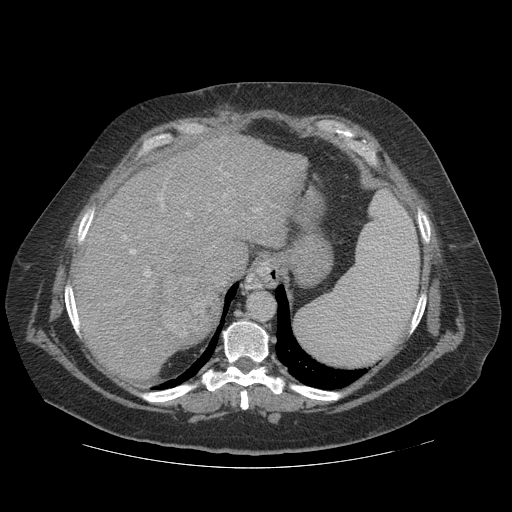
Contrast-enhanced abdominal CT (liver protocol), one axial slice. Position 90 of 121 along the scan axis. 140 kVp. Soft-tissue window (W 400 / L 40 HU). 2.5 mm slice thickness. 512 × 512 image matrix, field of view 420 × 420 mm. Case-level facts recorded for this patient, not image findings: diagnosis: hepatocellular carcinoma (patient treated with transarterial chemoembolisation; whether this scan precedes or follows treatment is not stated here); TNM stage (as recorded): Stage-IIIA; Child-Pugh class: A; tumour nodularity: multinodular; tumour size: 7.4 cm.
Outlined on this slice (semi-automatic segmentation, software-assisted and operator-edited):
- liver parenchyma outside the tumour (the mass and vessels are separate outlines, so this box may not span the whole liver): bounding box <74,134,308,380> (left, top, right, bottom; pixels)
- mass: <150,264,220,350>
- liver vessels: <116,167,274,292>